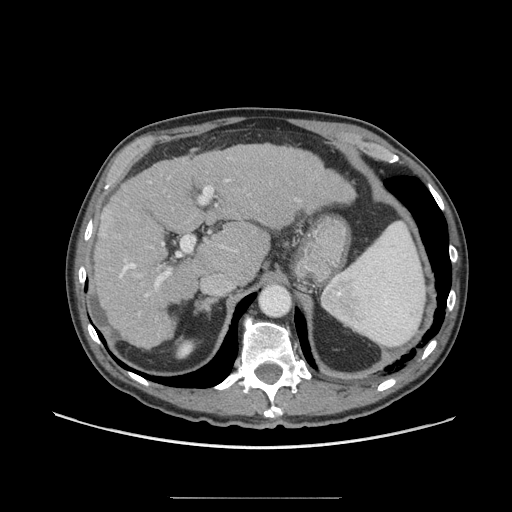
Contrast-enhanced abdominal CT (liver protocol), one axial slice. Slice 45 of 71 in the series (ordered by position). Soft-tissue window (W 400 / L 40 HU). 2.5 mm slice thickness. 512 × 512 image matrix, field of view 400 × 400 mm. Case-level facts recorded for this patient, not image findings: diagnosis: hepatocellular carcinoma (patient treated with transarterial chemoembolisation; whether this scan precedes or follows treatment is not stated here); TNM stage (as recorded): Stage-I; Child-Pugh class: A; tumour nodularity: uninodular; tumour size: 3.5 cm.
Outlined on this slice (semi-automatic segmentation, software-assisted and operator-edited):
- liver parenchyma outside the tumour (the mass and vessels are separate outlines, so this box may not span the whole liver): bounding box [x1, y1, x2, y2] px = [94, 144, 340, 347]
- mass: [100, 209, 130, 241]
- liver vessels: [119, 179, 230, 297]